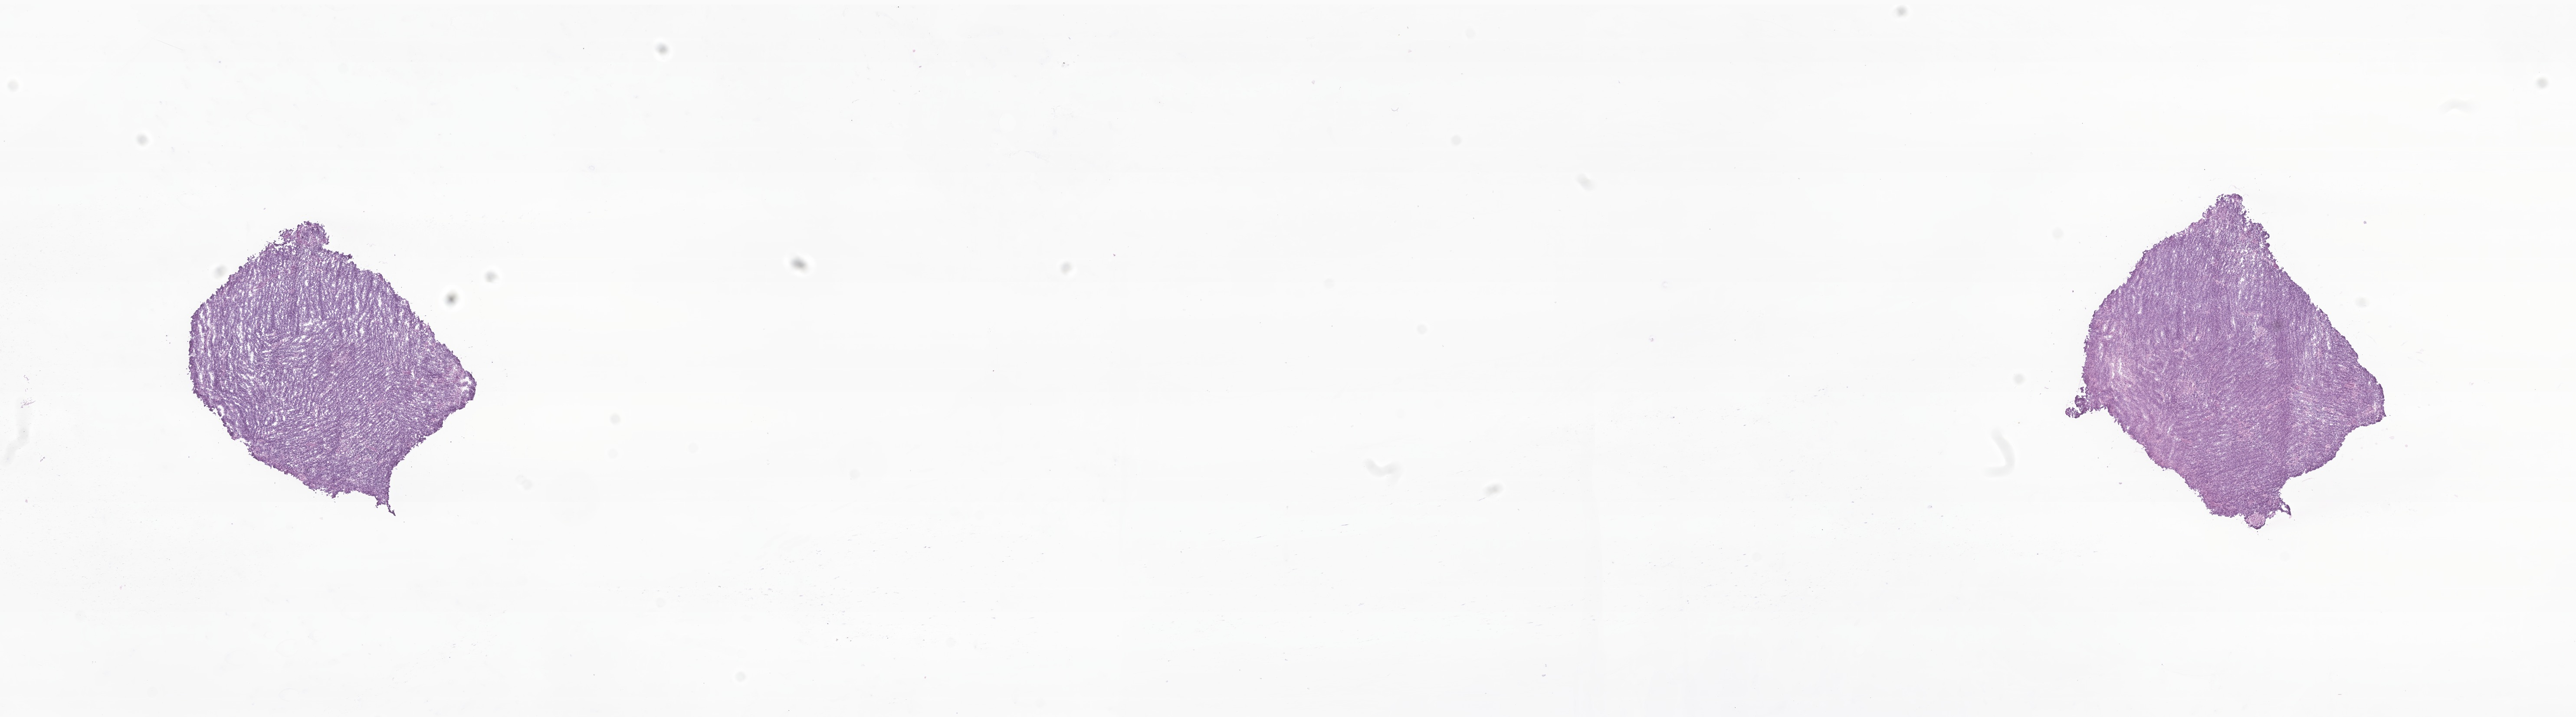
Digitized hematoxylin and eosin (H&E)-stained section of tumor tissue from the brain — whole scanned area (about 25.0 x 7.0 mm) shown as a low-resolution overview. Cryosection (OCT / tissue freezing medium). Female patient, age 174 months (14 years 6 months).
- diagnosis: Medulloblastoma, NOS